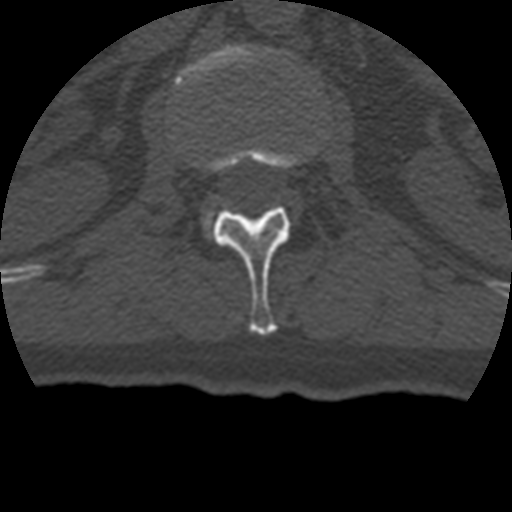
CT including the spine, one axial slice. Slice 136 of 399 in the series (ordered by position). Reconstruction kernel STANDARD. Bone window (W 1800 / L 400 HU). 1.25 mm slice thickness. 512 × 512 image matrix, field of view 160 × 160 mm. Patient age 69 years. From the clinical record (not read from this slice): primary cancer: prostate.
Structures marked on this image (semi-automatic segmentation, software-assisted and operator-edited):
- L1 vertebra: box from (x=206, y=143) to (x=316, y=335) px
- L2 vertebra: (x=174, y=44)–(x=283, y=89)